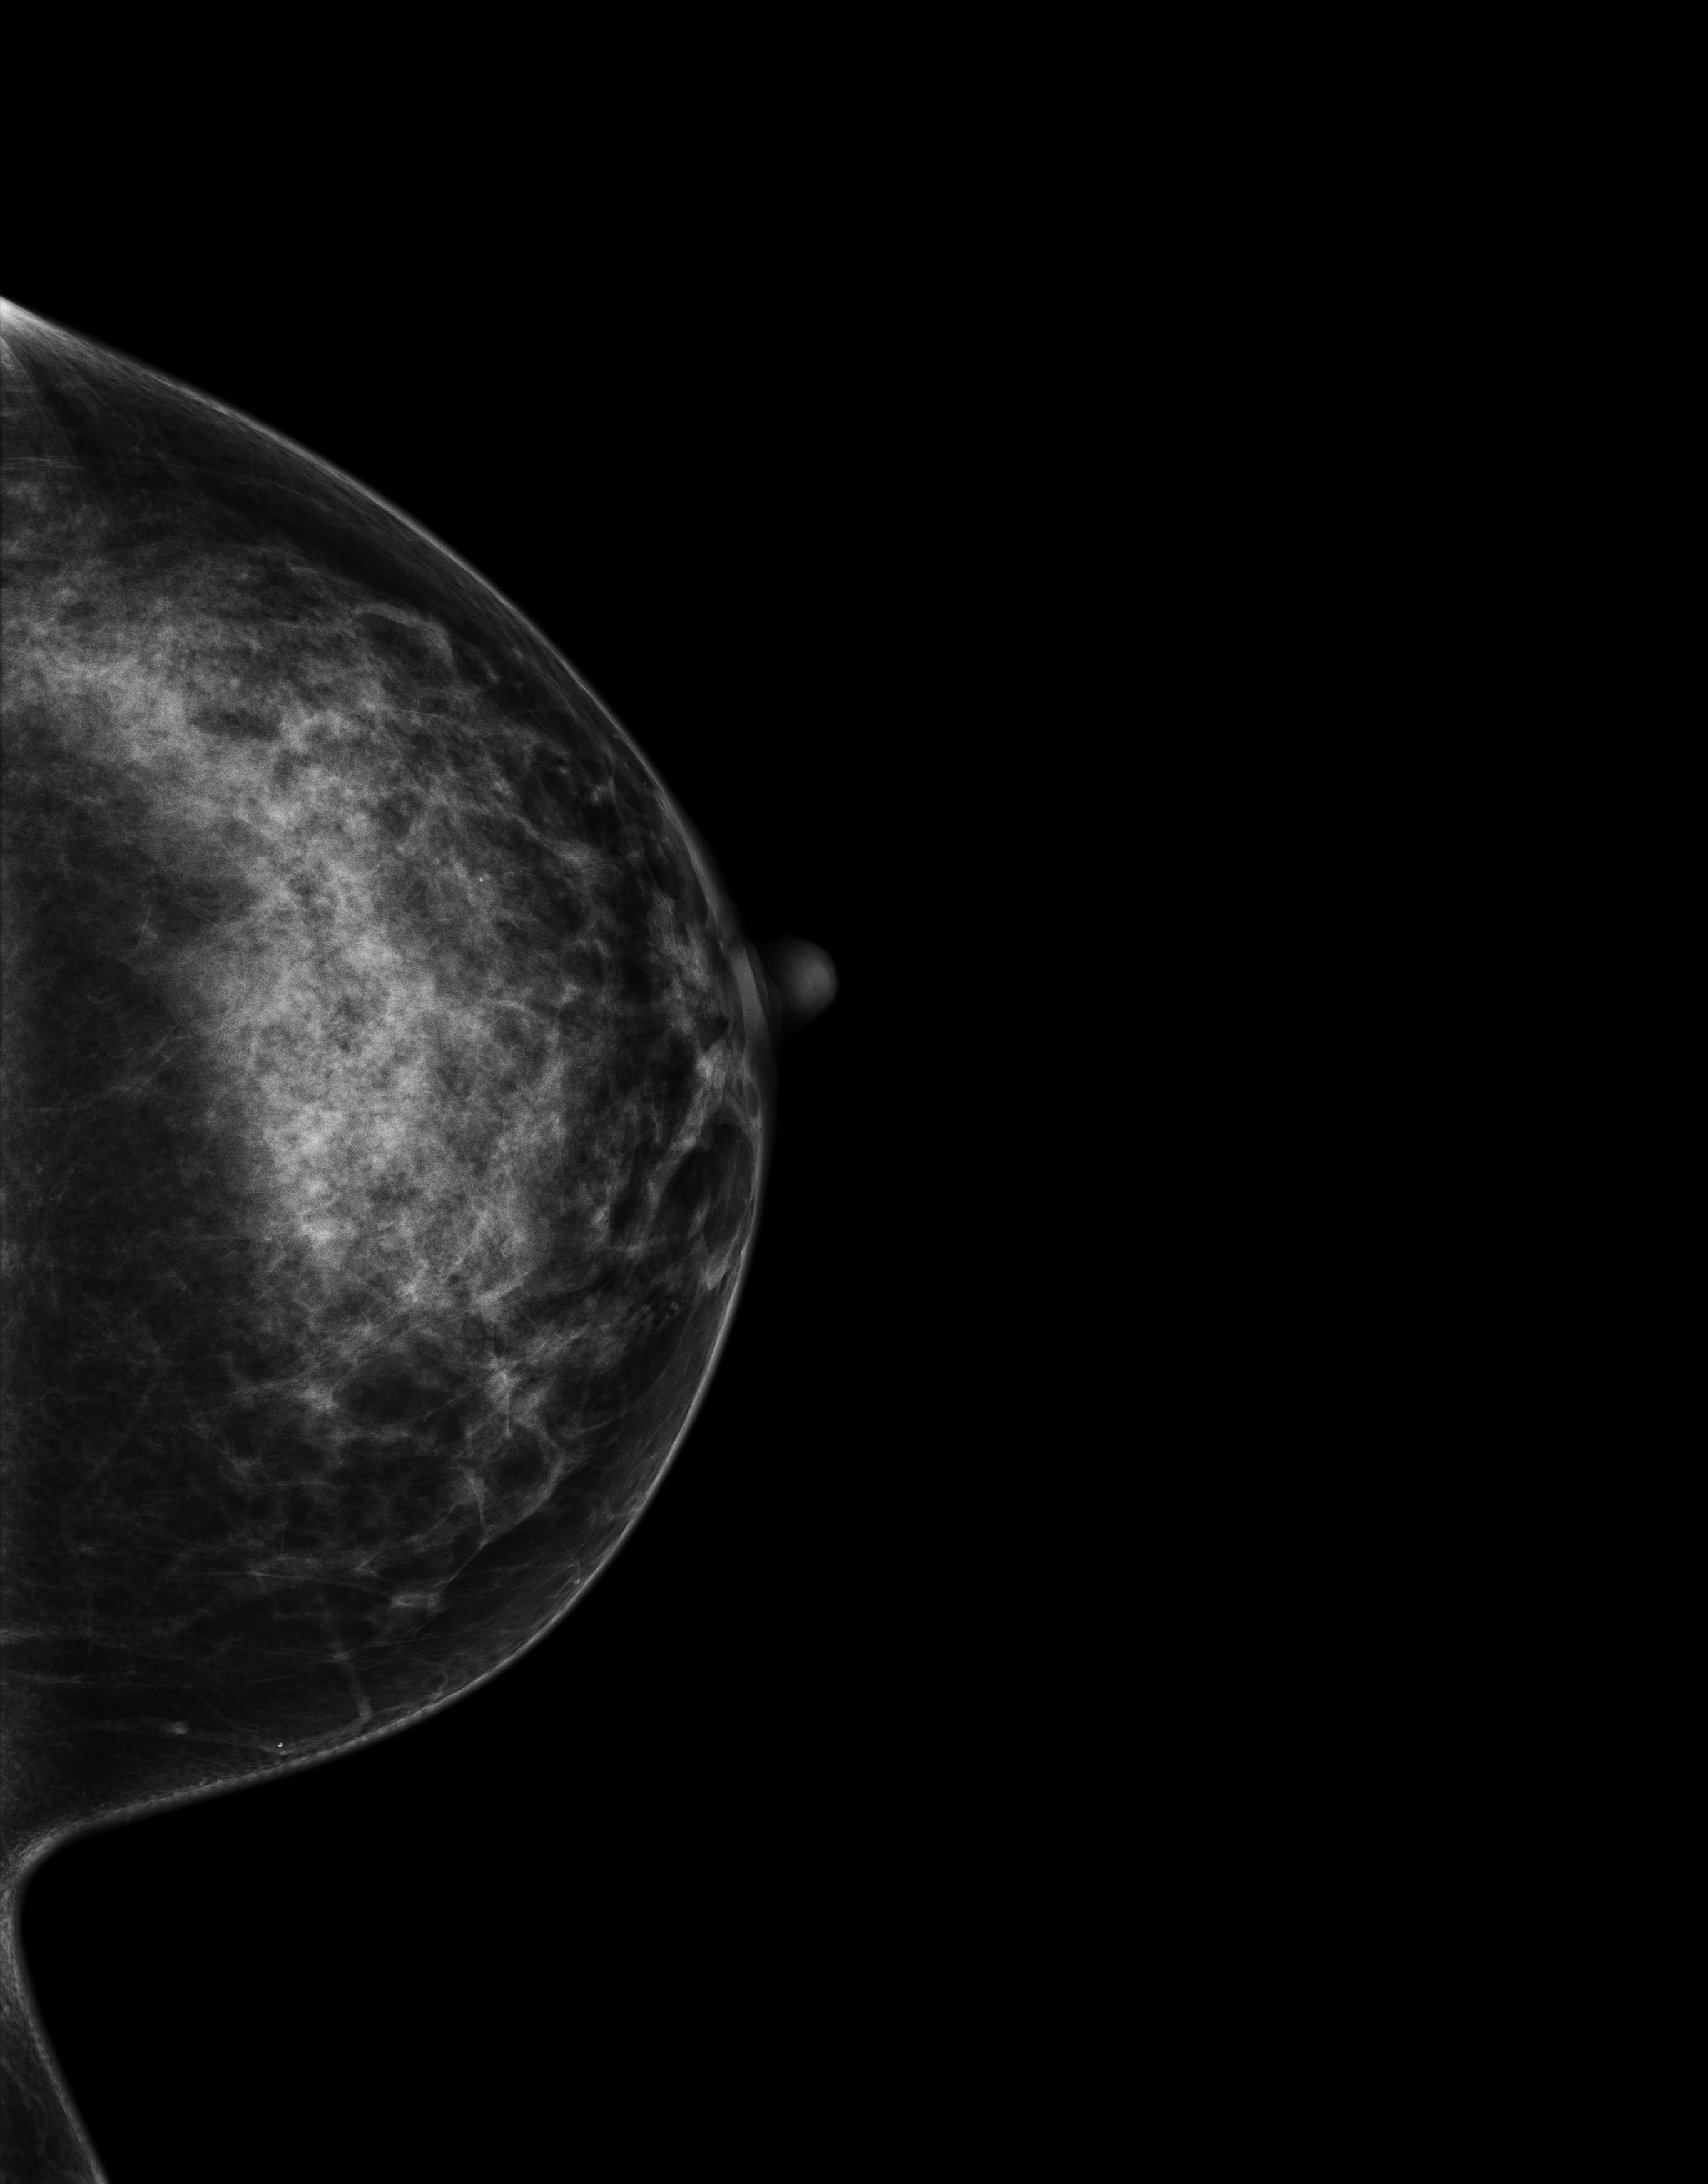
Annual screening mammography examination. Patient: female, 49 years.
Image type: full-field digital mammogram. Breast: left. Projection: cranio-caudal projection. Breast density at the screening exam (both breasts): heterogeneously dense (BI-RADS density category c). Final BI-RADS assessment for this screening round (tomosynthesis exam, both breasts): category 1. Recall: no recall after this screen.